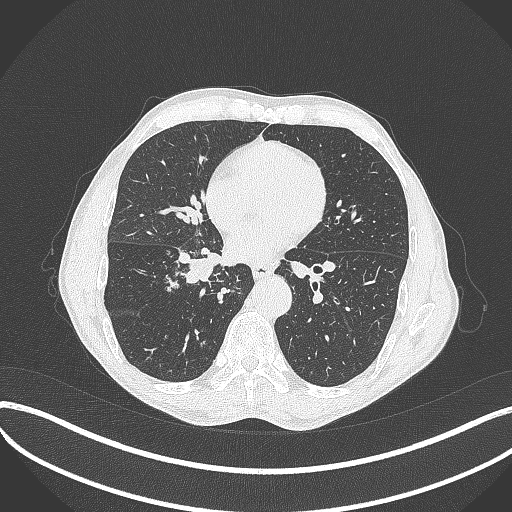
Chest CT, one axial slice; position 189 of 481 along the scan axis; reconstruction kernel B70f; lung window (W 1500 / L -600 HU); 1 mm slice thickness; 512 × 512 image matrix, field of view 400 × 400 mm. Patient: male, 65 years. Case-level facts recorded for this patient, not image findings: clinical TNM (as recorded): T2a N0 M0.
Outlined on this slice (bounding box drawn by a radiologist):
- lung tumour (recorded histology: squamous cell carcinoma): box from (x=174, y=252) to (x=226, y=288) px